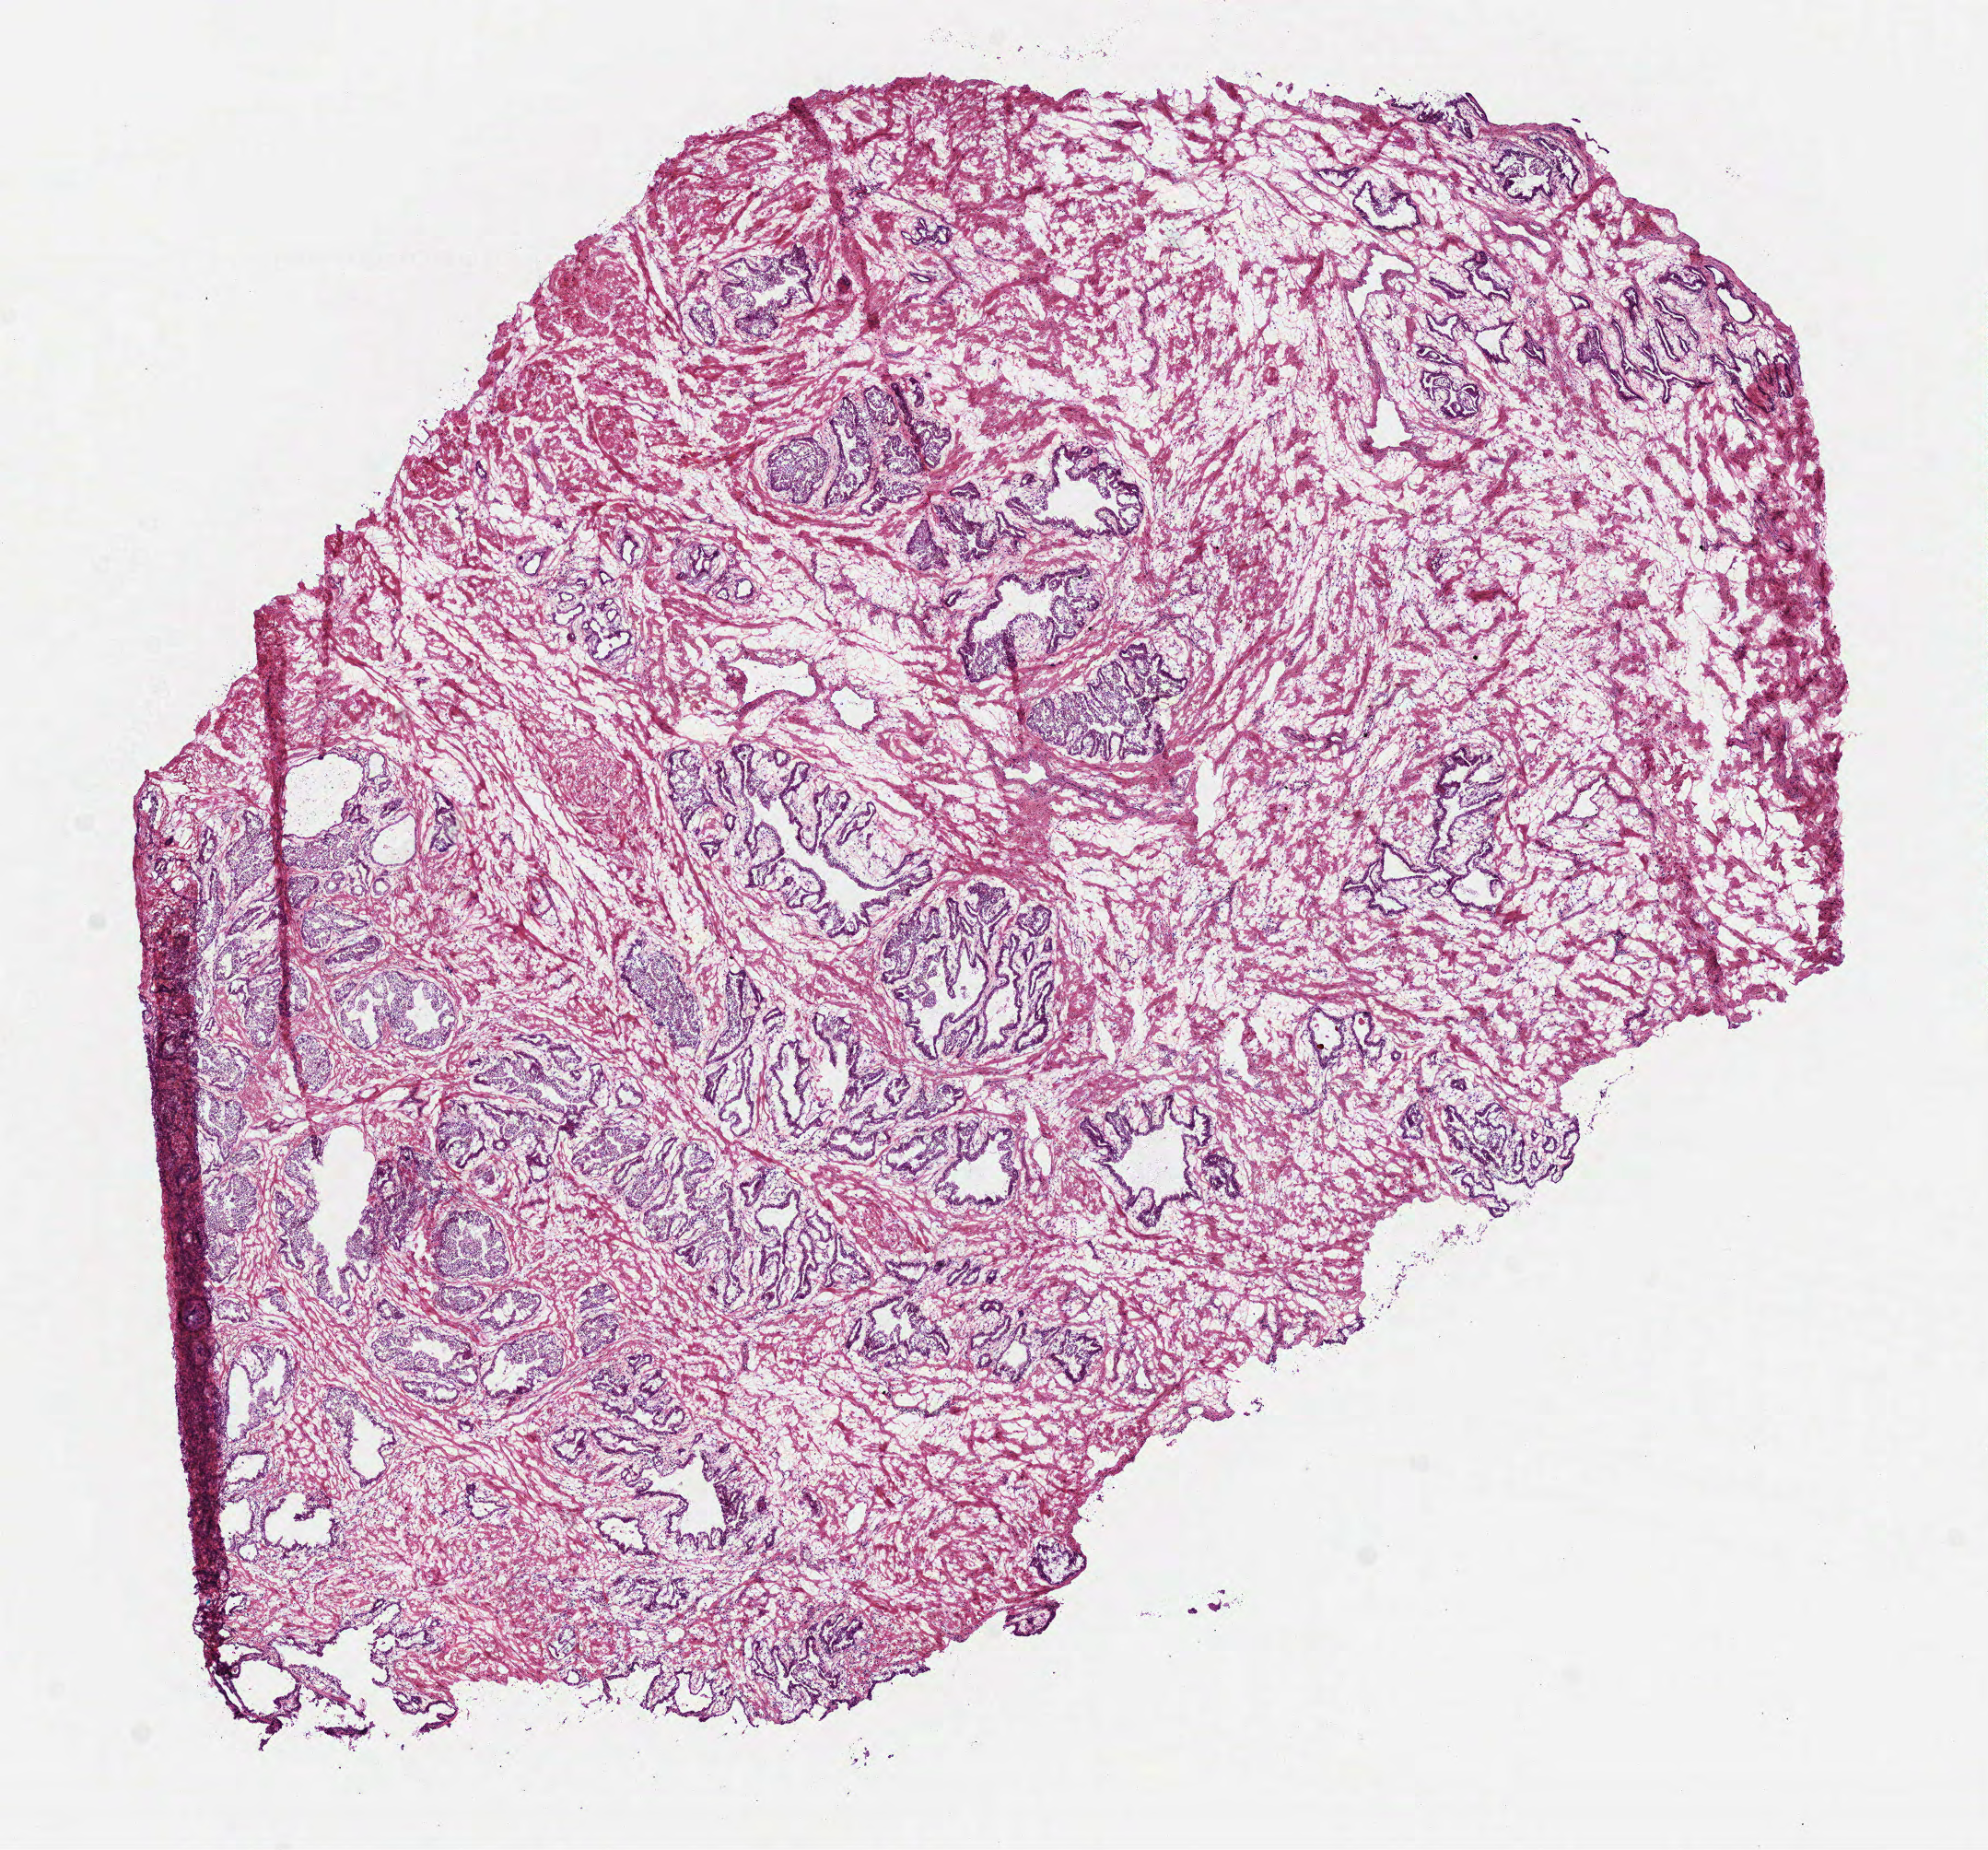
Whole-slide histology image, H&E — shown as a low-resolution overview of the whole scanned area (about 8.7 x 8.1 mm), frozen section, sample: solid tissue normal (non-tumour tissue), prostate. Male patient; age at initial diagnosis 49 years.
This section: solid tissue normal (non-tumour) sample from the same patient. Patient diagnosis: Acinar cell carcinoma (prostate gland).